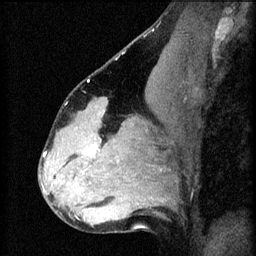
Breast MRI (dynamic contrast-enhanced), one sagittal slice. Position 36 of 60 along the scan axis. 3 images stored at this slice position (order not interpretable as contrast timing). 1.5 T. TE 4.2 ms, TR 8.2 ms. 2.3 mm slice thickness. 256 × 256 image matrix, field of view 180 × 180 mm. Female patient, age 37 years.
Outlined on this slice (semi-automatic segmentation, software-assisted and operator-edited):
- analysis volume of interest (the breast-tissue region the enhancement analysis was run in; not a lesion): bounding box [x1, y1, x2, y2] px = [67, 120, 122, 179]
- tumour enhancement mask (voxels above the 70 % enhancement threshold inside the analysis volume of interest): [86, 138, 101, 155]